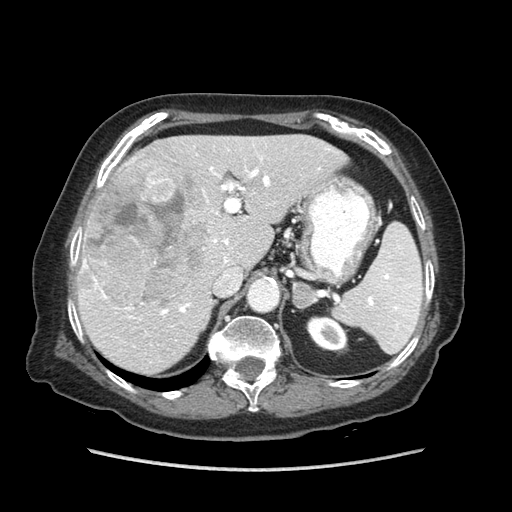
Contrast-enhanced abdominal CT (liver protocol), one axial slice. Position 53 of 89 along the scan axis. Reconstruction kernel STANDARD. Soft-tissue window (W 400 / L 40 HU). 2.5 mm slice thickness. 512 × 512 image matrix. Case-level facts recorded for this patient, not image findings: diagnosis: hepatocellular carcinoma (patient treated with transarterial chemoembolisation; whether this scan precedes or follows treatment is not stated here); TNM stage (as recorded): Stage-IIIA; Child-Pugh class: A; tumour nodularity: multinodular; tumour size: 11 cm.
Structures marked on this image (semi-automatically segmented with operator editing):
- liver parenchyma outside the tumour (the mass and vessels are separate outlines, so this box may not span the whole liver): bounding box (x1, y1, x2, y2) in pixels: (78, 134, 348, 374)
- mass: (85, 157, 209, 306)
- liver vessels: (83, 148, 330, 317)